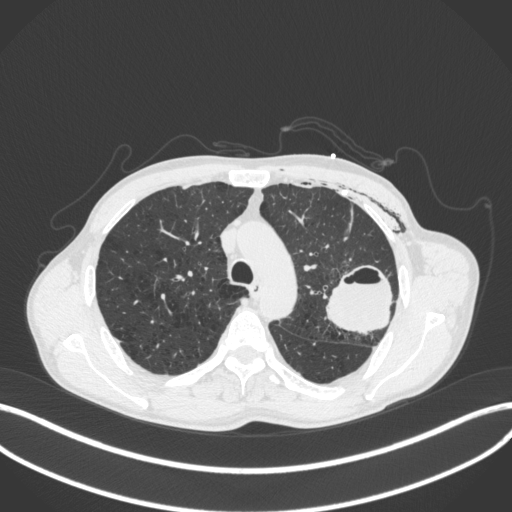
Chest CT, one axial slice. Slice 291 of 416 in the series (ordered by position). 120 kVp. Lung window (W 1500 / L -600 HU). 1 mm slice thickness. 512 × 512 image matrix, field of view 400 × 400 mm. Male patient, age 58 years. From the clinical record (not read from this slice): clinical TNM (as recorded): T3 N0 M0.
Annotated regions visible in this slice (rectangle marked by the reading radiologist):
- lung tumour (recorded histology: adenocarcinoma): bounding box (x1, y1, x2, y2) in pixels: (326, 262, 396, 336)